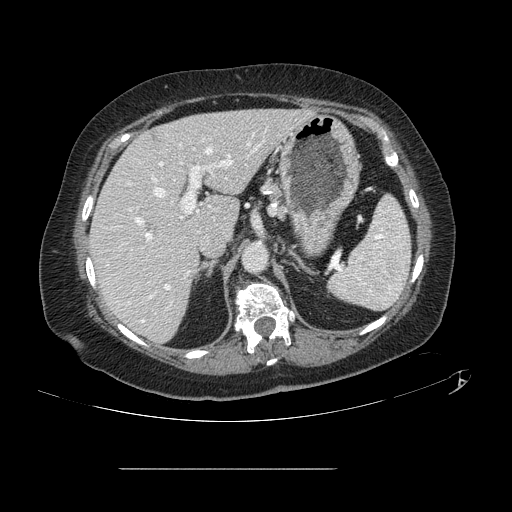
Contrast-enhanced abdominal CT, one axial slice. Slice 84 of 148 in the series (ordered by position). 120 kVp. Intravenous contrast given. Soft-tissue window (W 400 / L 40 HU). 512 × 512 image matrix, field of view 439 × 439 mm. Female patient, age 75 years. From the clinical record (not read from this slice): diagnosis: colorectal cancer liver metastases, imaged before liver resection; multiple liver metastases: no; largest metastasis: 2.4 cm.
Outlined on this slice (manually delineated by an expert):
- hepatic veins: bounding box <142,148,212,322> (left, top, right, bottom; pixels)
- liver: <90,110,309,342>
- planned liver remnant (the part of the liver to remain after resection): <90,109,309,342>
- portal vein (with intrahepatic branches): <136,133,265,289>
- liver metastasis: <152,134,160,142>